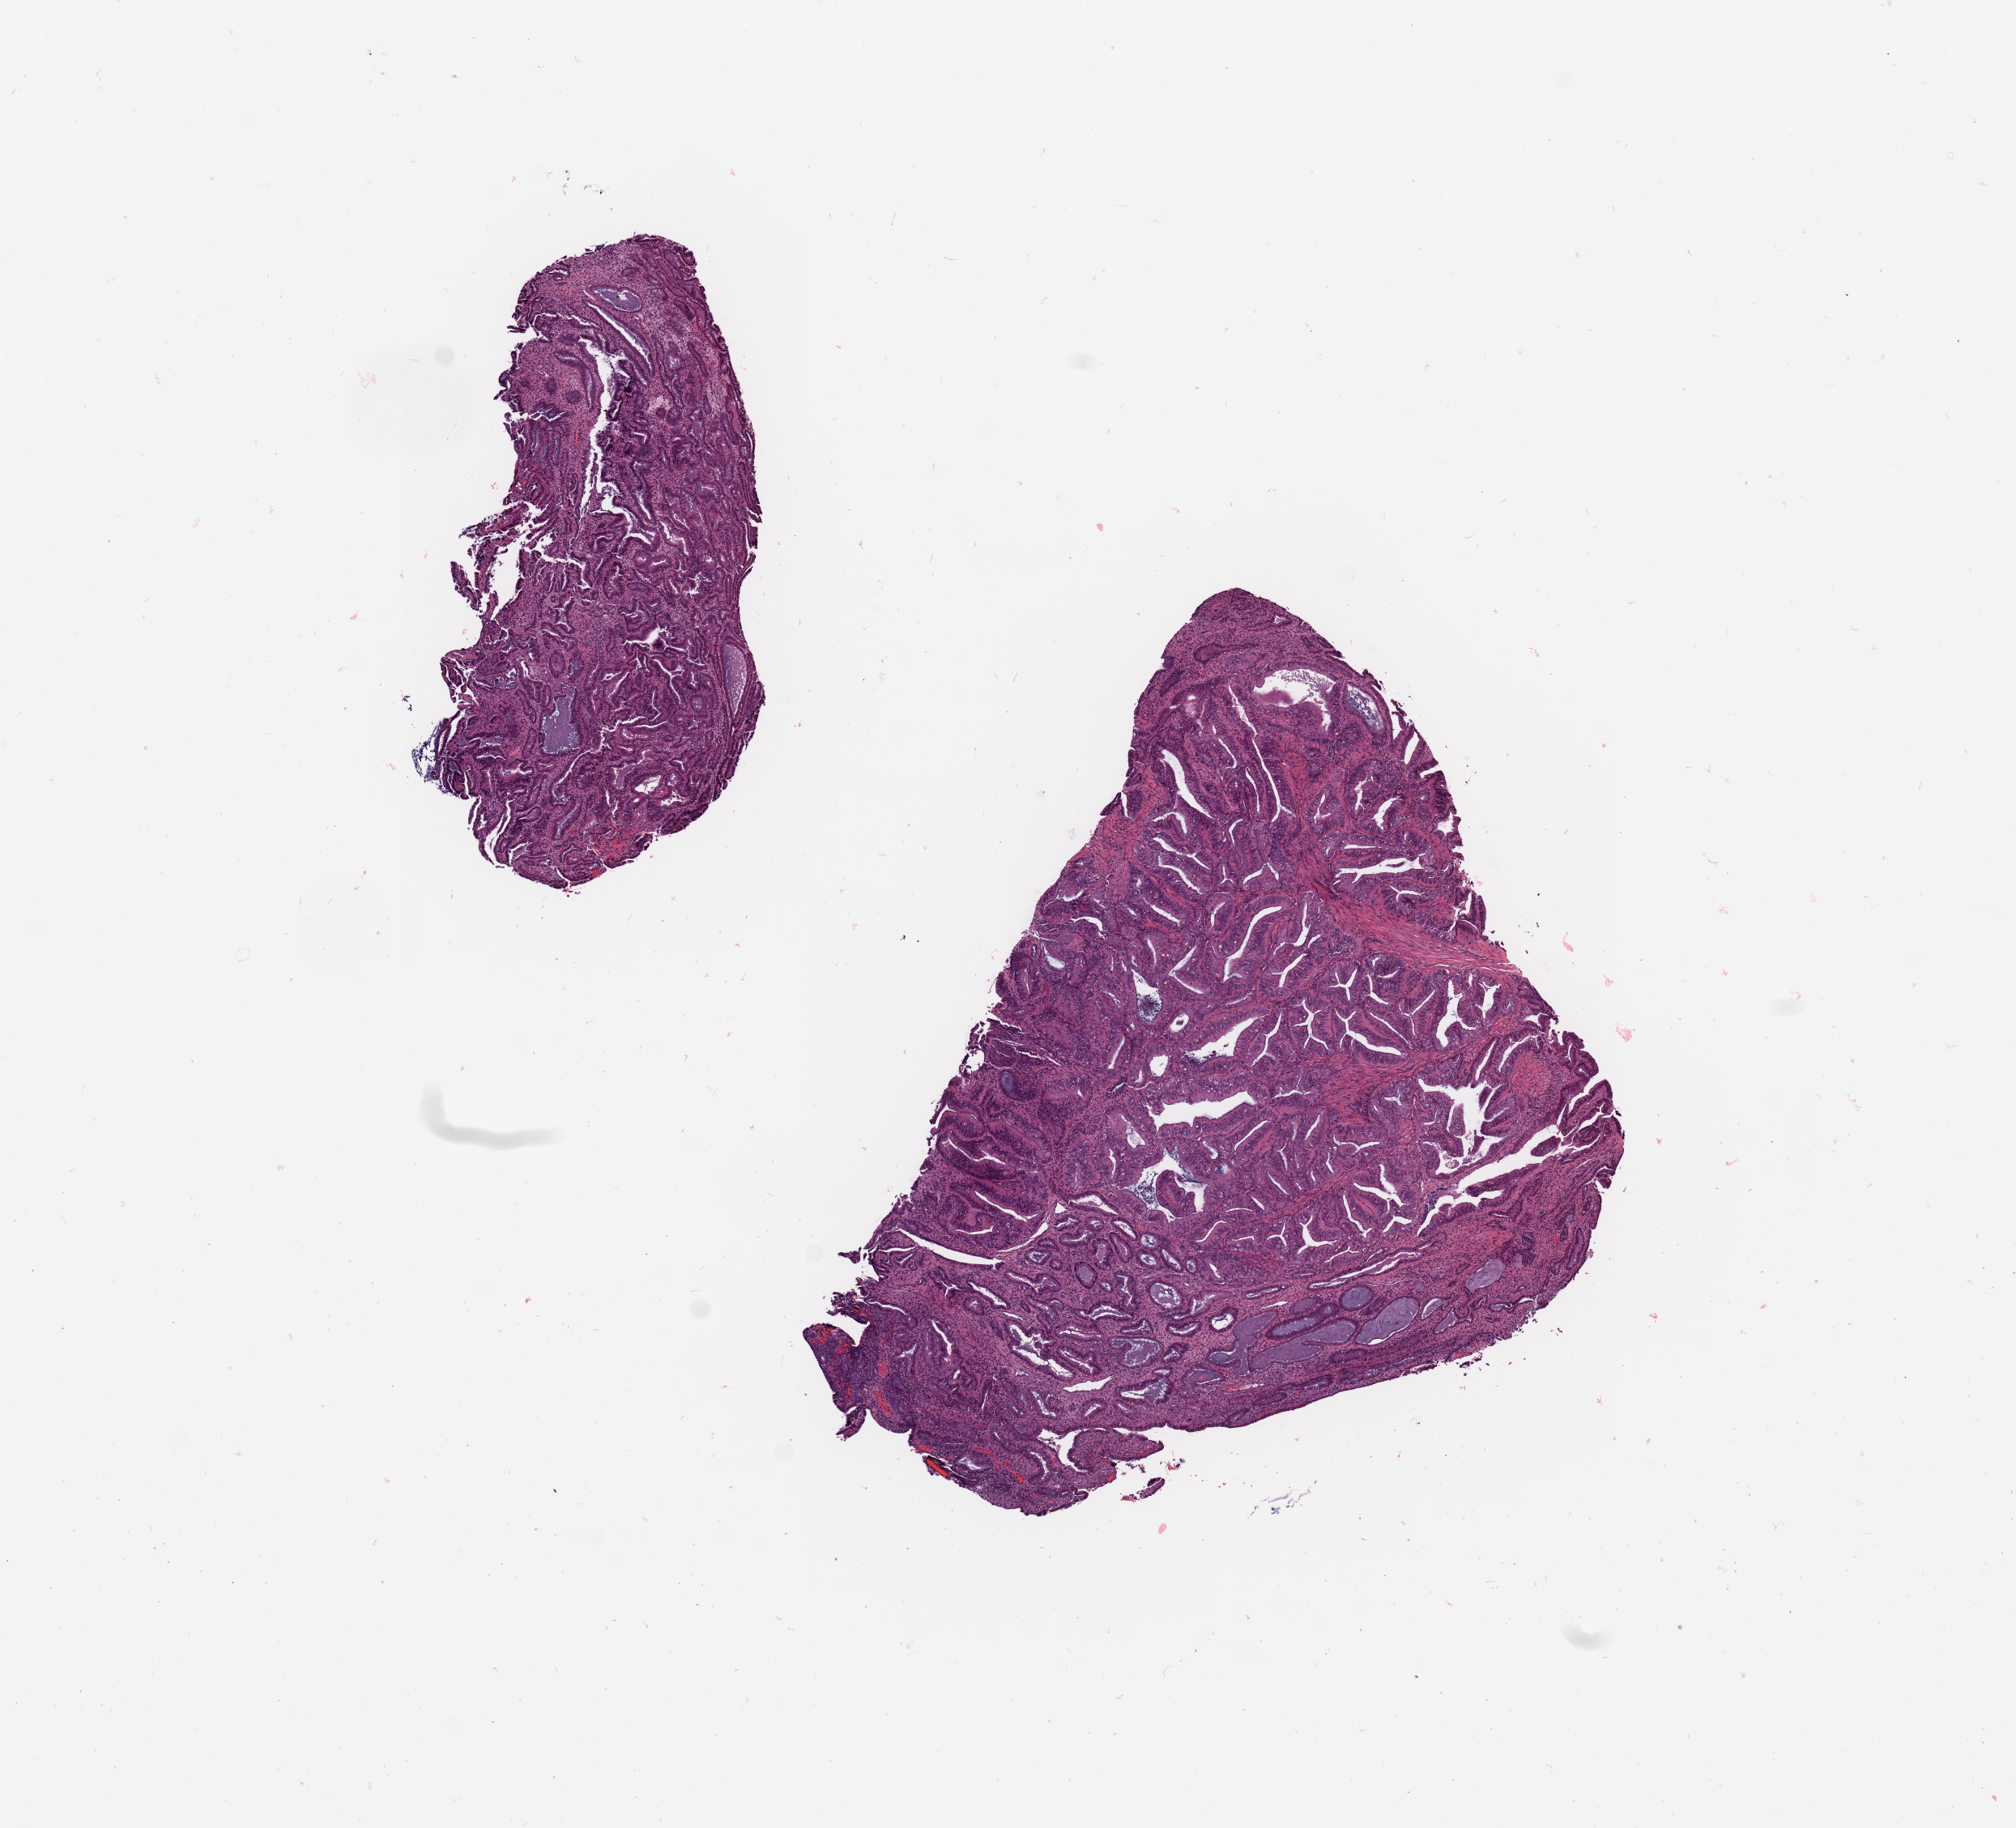
Digitized H&E tissue section (whole slide), shown as a low-resolution overview of the whole scanned area (about 9.8 x 8.9 mm). Tumour tissue sample, sampled site: uterus. 56-year-old female patient. Histologic grade: G1 (well differentiated). Composition of this section per pathologist review: tumour nuclei 80%, necrosis 0%.
AJCC pathologic stage: II. Diagnosis: Endometrioid adenocarcinoma, NOS.